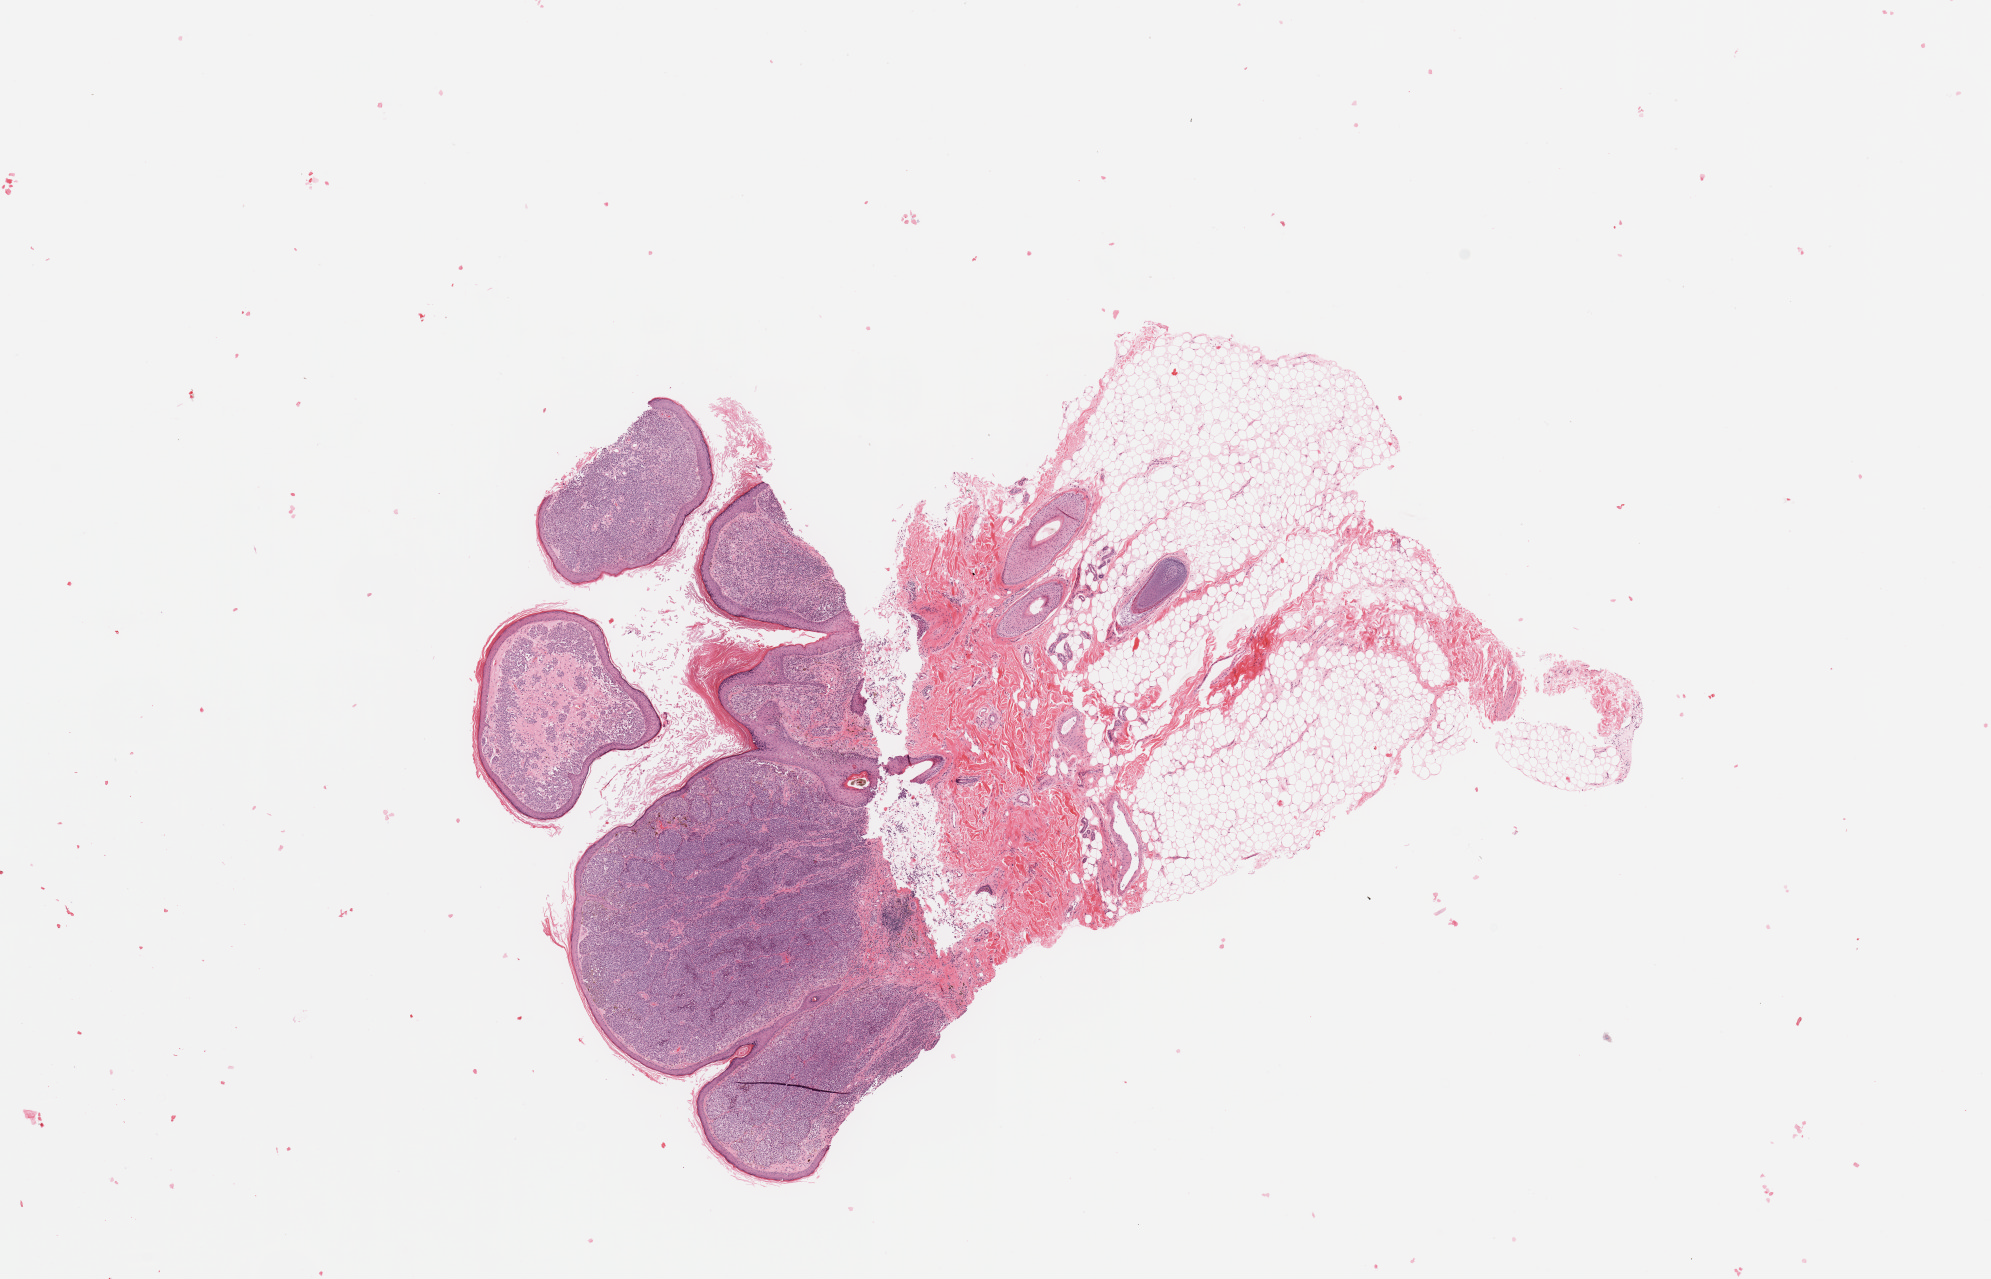
Whole-slide histology image, Hematoxylin and eosin (H&E) stained — whole scanned area (about 15.8 x 10.1 mm, acquisition: 20x scan) shown as a low-resolution overview, melanoma tumour tissue; sampled site not recorded. 73-year-old female patient.
Primary tumour site (as recorded): head & neck. AJCC pathologic stage: IIA. Diagnosis: Malignant melanoma, NOS.